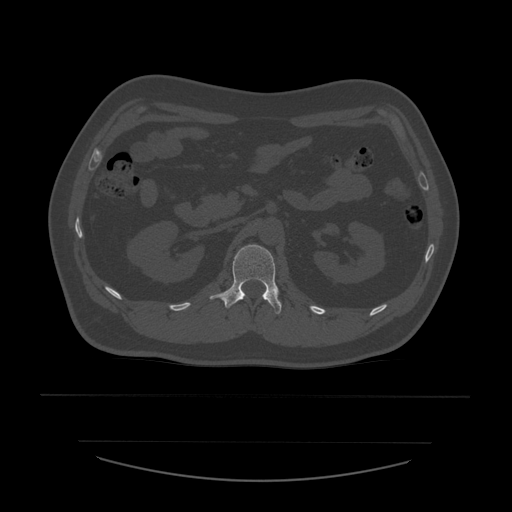
CT including the spine, one axial slice. Slice 230 of 532 in the series (ordered by position). Reconstruction kernel STANDARD. 120 kVp. Bone window (W 1800 / L 400 HU). 512 × 512 image matrix, field of view 441 × 441 mm. Patient age 44 years. From the clinical record (not read from this slice): primary cancer: soft tissue sarcoma.
Outlined on this slice (semi-automatic segmentation, software-assisted and operator-edited):
- L1 vertebra: bounding box [x1, y1, x2, y2] px = [210, 245, 282, 315]